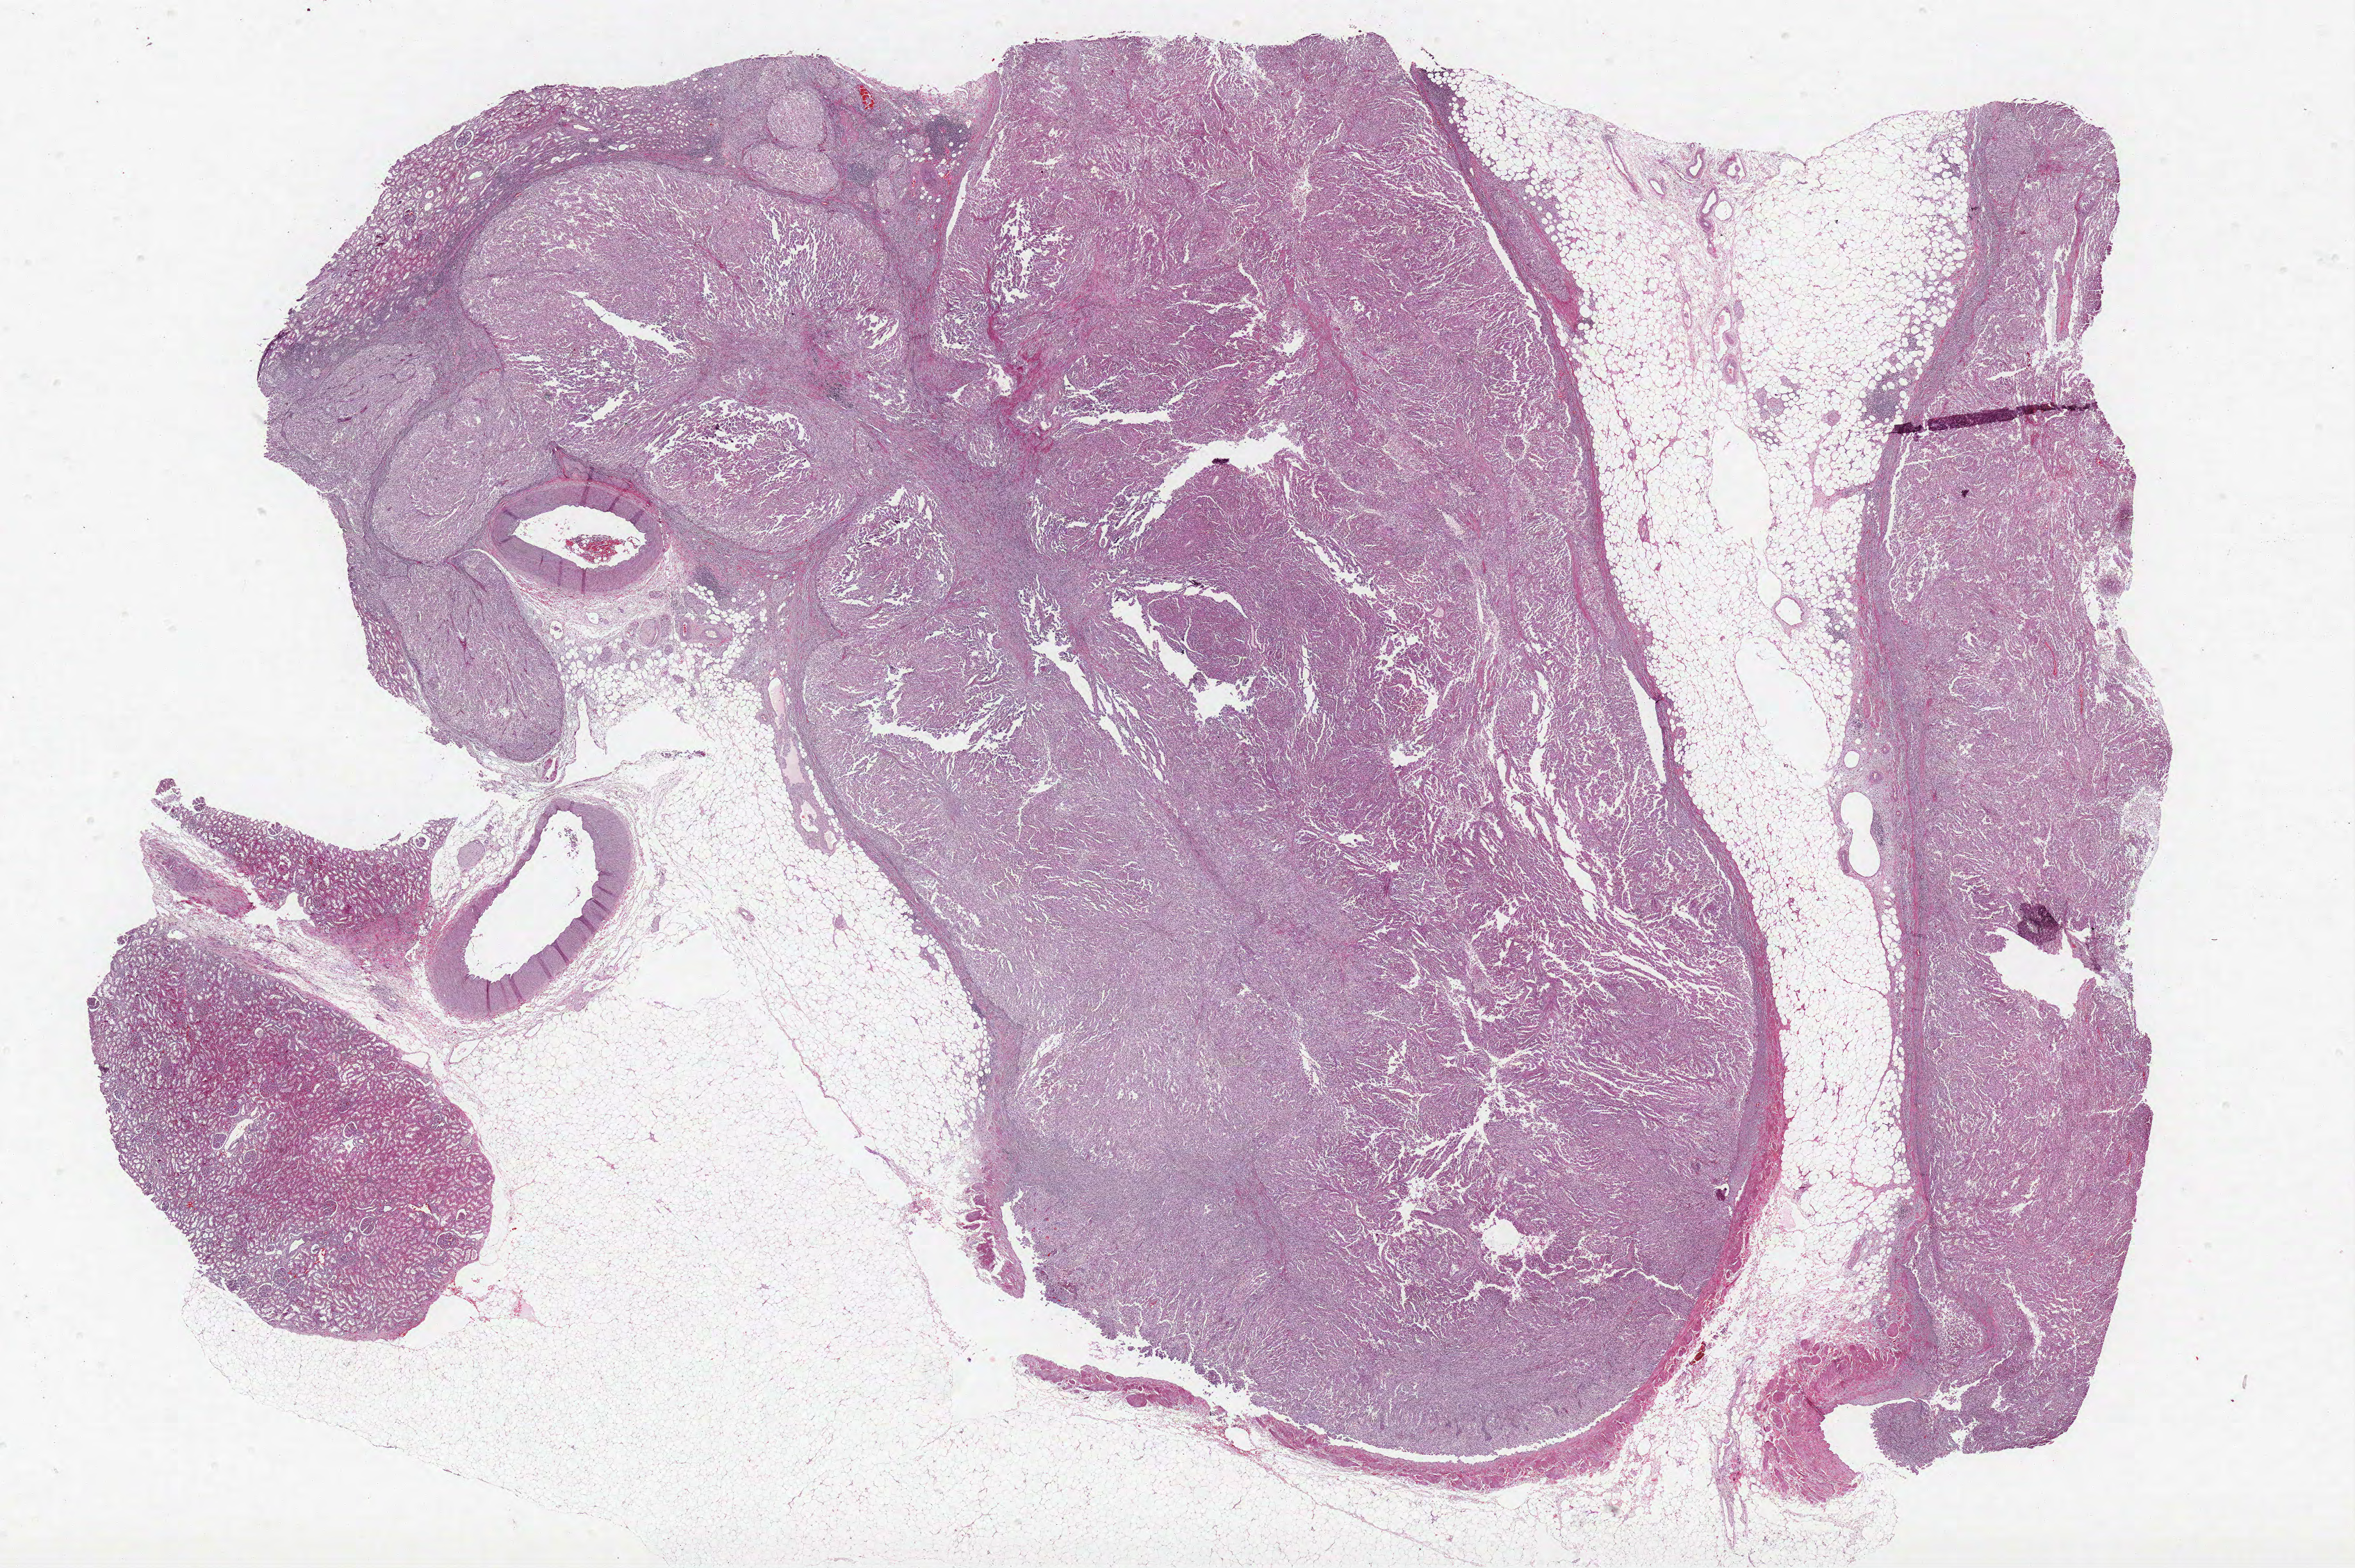
Digitized Hematoxylin and eosin (H&E) stained tissue section (whole slide) — a low-resolution overview of the entire scanned area, about 27.1 x 18.0 mm (acquisition: 40x scan); FFPE section; kidney, primary tumour sample. Patient: male, age at initial diagnosis 60 years.
Histologic diagnosis: Papillary adenocarcinoma, NOS.